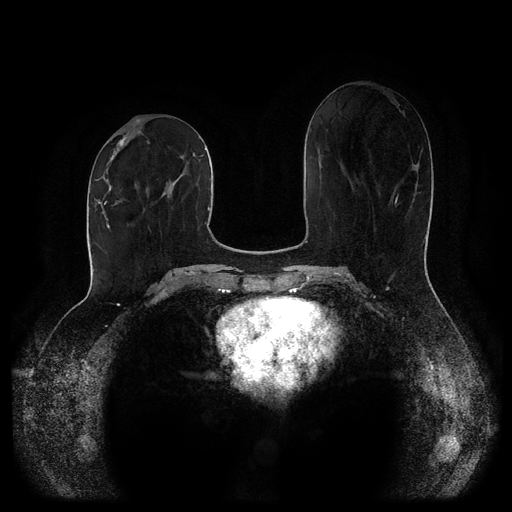
Breast MRI (dynamic contrast-enhanced, multi-phase), one axial slice. Position 44 of 116 along the scan axis. Dynamic contrast-enhanced series, time point 2 of 5 at this slice position (early post-contrast). 1.5 T. TE 2.6 ms, TR 5.2 ms. 2 mm slice thickness. 512 × 512 image matrix. Patient: female, 52 years.
Structures marked on this image (semi-automatic segmentation, software-assisted and operator-edited):
- breast lesion (labelled 'tumour' in the annotation; benign lesions carry a separate 'benign' label): box from (x=99, y=134) to (x=128, y=182) px